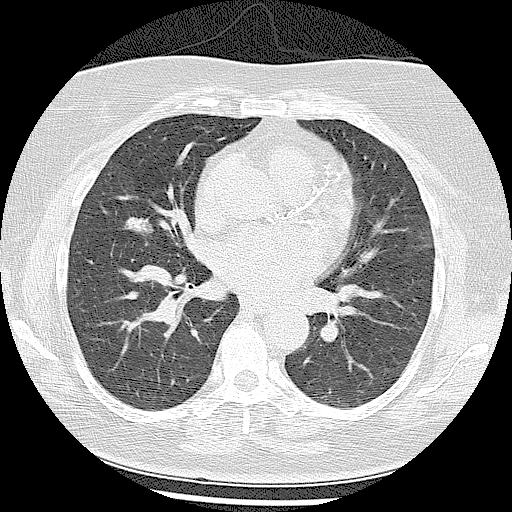
Chest CT (low-dose screening protocol), one axial image; first (baseline) screen; lung window (W 1500 / L -600 HU); 120 kVp; 512 × 512 image matrix. Female, age 57 years at enrolment.
Lesion marked by an expert reader, bounding box [x1, y1, x2, y2] px = [104, 199, 167, 253]. The screening reader recorded 4 non-calcified nodules or masses ≥4 mm on this exam; which of them this box marks is not recorded. Lung cancer was diagnosed 87 days after this screen: adenocarcinoma, NOS, right middle lobe, well differentiated (G1), stage IA (AJCC 6th edition), 21 mm at pathology.